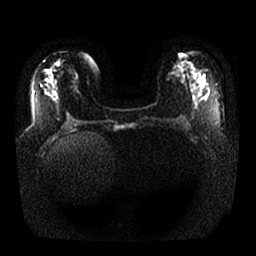
Breast MRI, one axial slice; position 11 of 25 along the scan axis; diffusion-weighted series; image 2 of 4 stored at this slice position (different b-values; order by instance number); 1.5 T; 4 mm slice thickness; 256 × 256 image matrix, field of view 350 × 350 mm. Female patient.
Outlined on this slice (expert manual segmentation):
- tumour on diffusion-weighted imaging: box from (x=193, y=81) to (x=204, y=92) px